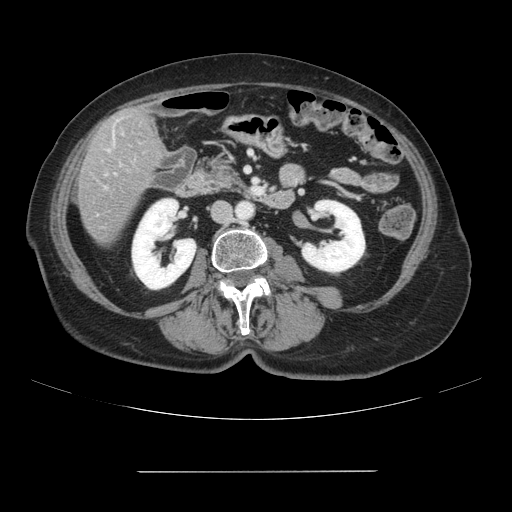
Contrast-enhanced abdominal CT, one axial slice. Position 21 of 111 along the scan axis. Intravenous contrast given. Soft-tissue window (W 400 / L 40 HU). 2.5 mm slice thickness. 512 × 512 image matrix, field of view 400 × 400 mm. Female patient, age 74 years. Case-level facts recorded for this patient, not image findings: diagnosis: colorectal cancer liver metastases, imaged before liver resection; multiple liver metastases: yes; largest metastasis: 1.1 cm; disease in both lobes: yes.
Structures marked on this image (manually delineated by an expert):
- liver: box from (x=78, y=105) to (x=165, y=244) px